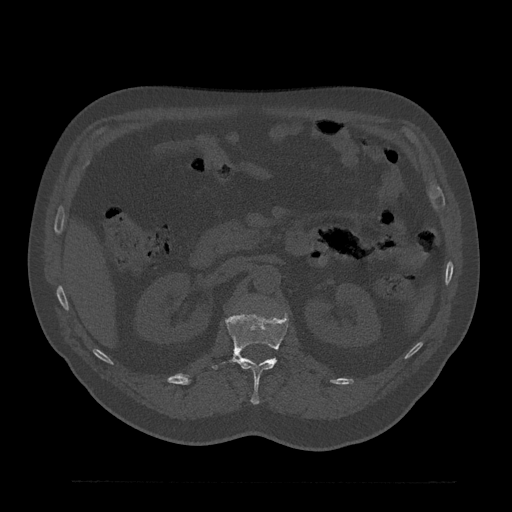
CT including the spine, one axial slice; reconstruction kernel Br40s/3; bone window (W 1800 / L 400 HU); 512 × 512 image matrix, field of view 430 × 430 mm. Male patient, age 61 years. Case-level facts recorded for this patient, not image findings: primary cancer: prostate.
Structures marked on this image (semi-automatic segmentation, software-assisted and operator-edited):
- L1 vertebra: bounding box [x1, y1, x2, y2] px = [210, 312, 288, 405]